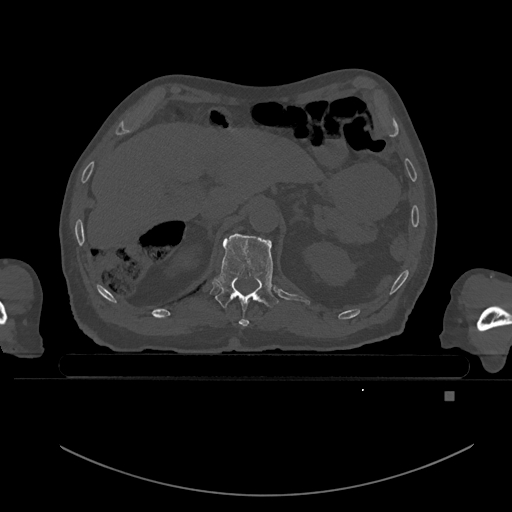
CT including the spine, one axial slice. Slice 32 of 969 in the series (ordered by position). Bone window (W 1800 / L 400 HU). 0.5 mm slice thickness. 512 × 512 image matrix, field of view 456 × 456 mm. Male patient, age 82 years. From the clinical record (not read from this slice): primary cancer: prostate; vertebrae with lytic lesions (as recorded): T11, T9, T8, T2.
Outlined on this slice (semi-automatic segmentation, software-assisted and operator-edited):
- T11 vertebra: bounding box [x1, y1, x2, y2] px = [214, 233, 278, 326]